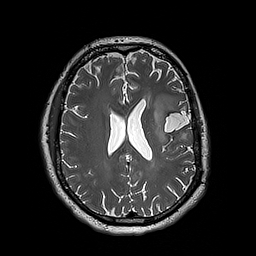
Brain MRI from a brain-tumour surgery series, one axial slice. Slice 84 of 192 in the series (ordered by position). 1 mm slice thickness. 256 × 256 image matrix. From the clinical record (not read from this slice): histopathology: Astrocytoma; WHO grade: 3; IDH mutation: yes.
Outlined on this slice (manually delineated by an expert):
- tumour: box from (x=153, y=94) to (x=179, y=145) px